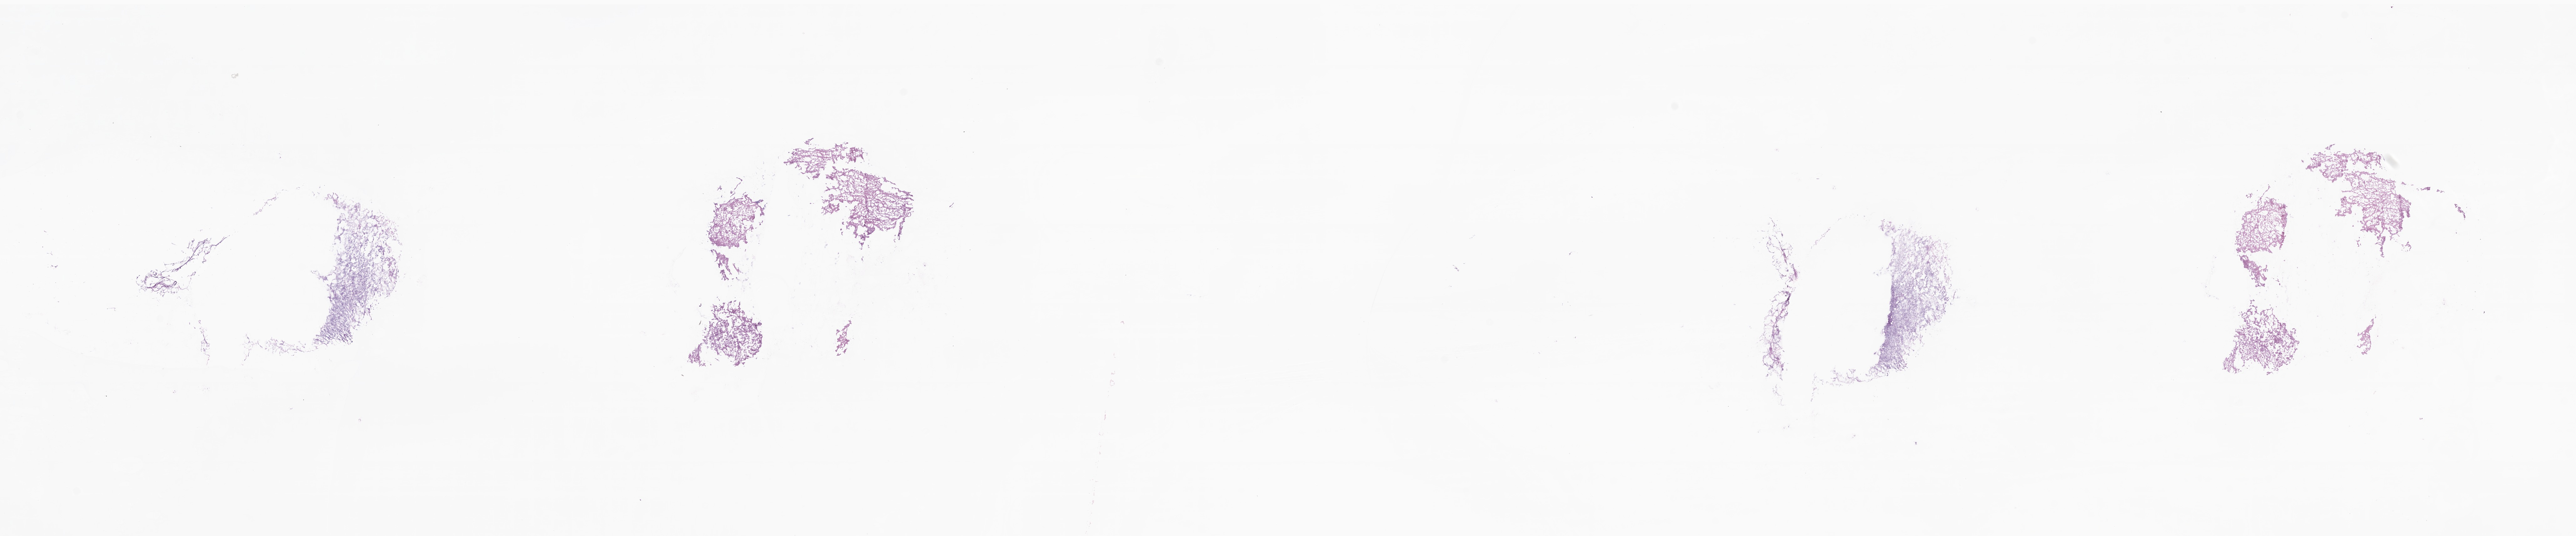
Whole-slide image, hematoxylin and eosin (H&E) stain — a low-resolution overview of the entire scanned area, about 34.7 x 7.2 mm; frozen section; specimen: metastatic tumor tissue, resected from lymph node. Female patient; age at initial diagnosis 50 years. Slide review estimates, as recorded: tumor cells 0%, tumor nuclei 0%, stromal cells 100%, necrosis 0%, normal cells 0%. Inflammatory infiltration, as recorded: lymphocyte infiltration 0%, monocyte infiltration 0%, neutrophil infiltration 0%.
Patient diagnosis (primary): Malignant melanoma, NOS. Section: top of the tissue portion.